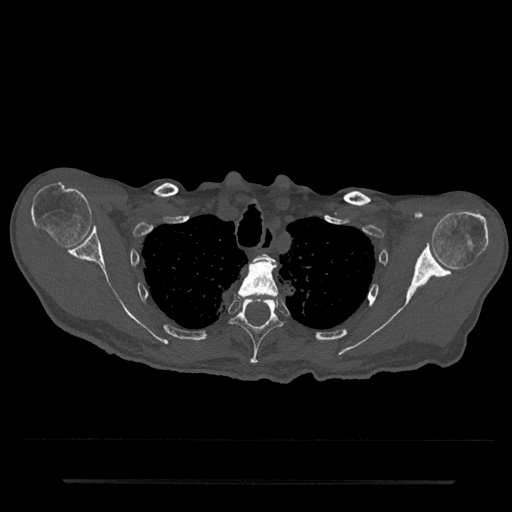
CT including the spine, one axial slice; slice 633 of 797 in the series (ordered by position); 120 kVp; bone window (W 1800 / L 400 HU); 0.5 mm slice thickness; 512 × 512 image matrix, field of view 427 × 427 mm. Male patient, age 74 years. From the clinical record (not read from this slice): primary cancer: prostate.
Structures marked on this image (semi-automatic segmentation, software-assisted and operator-edited):
- T2 vertebra: bounding box [x1, y1, x2, y2] px = [255, 253, 274, 262]
- T3 vertebra: [238, 259, 279, 296]
- T4 vertebra: [231, 298, 282, 365]